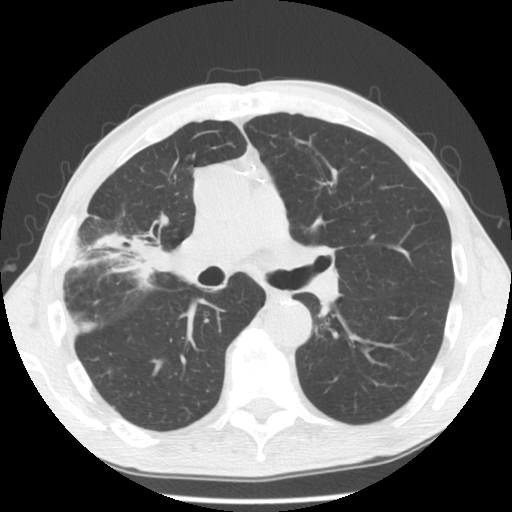
Low-dose screening chest CT, one axial slice; slice 77 of 132 in the series (ordered by position); lung window (W 1500 / L -600 HU); 512 × 512 image matrix, field of view 334 × 334 mm.
Outlined on this slice (manually delineated by an expert):
- lesion 1 (tumor, hilum of right lung): bounding box [x1, y1, x2, y2] px = [128, 241, 174, 275]